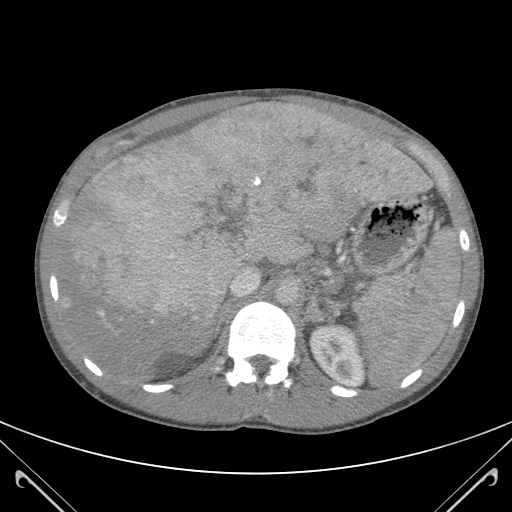
Contrast-enhanced abdominal CT (liver protocol), one axial slice. Slice 78 of 118 in the series (ordered by position). 120 kVp. Soft-tissue window (W 400 / L 40 HU). 3 mm slice thickness. 512 × 512 image matrix, field of view 380 × 380 mm. Case-level facts recorded for this patient, not image findings: diagnosis: hepatocellular carcinoma (patient treated with transarterial chemoembolisation; whether this scan precedes or follows treatment is not stated here); TNM stage (as recorded): Stage-IIIB.
Annotated regions visible in this slice (semi-automatically segmented with operator editing):
- abdominal aorta: bounding box (x1, y1, x2, y2) in pixels: (275, 281, 298, 306)
- liver parenchyma outside the tumour (the mass and vessels are separate outlines, so this box may not span the whole liver): (58, 107, 423, 378)
- mass: (75, 108, 424, 345)
- liver vessels: (99, 107, 386, 316)